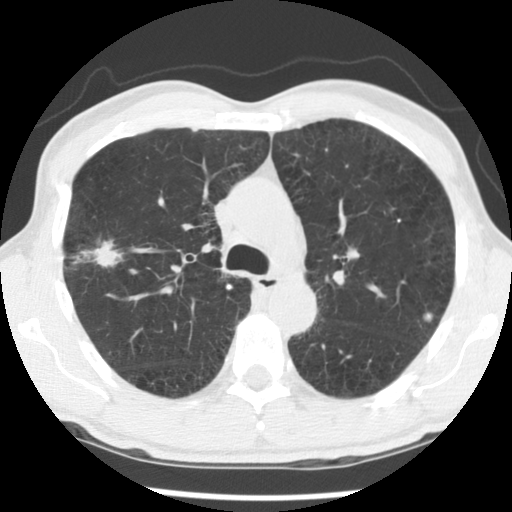
Low-dose screening chest CT, one axial slice; slice 88 of 138 in the series (ordered by position); reconstruction kernel STANDARD; 140 kVp; lung window (W 1500 / L -600 HU); 2.5 mm slice thickness; 512 × 512 image matrix.
Structures marked on this image (expert manual segmentation):
- lesion 1 (tumor, upper lobe of right lung): box from (x=73, y=240) to (x=123, y=267) px